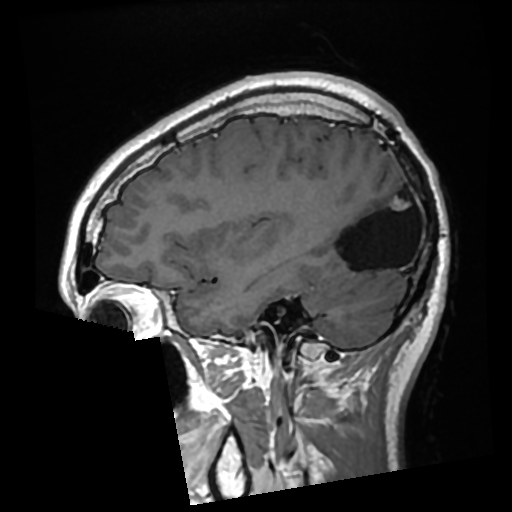
Brain MRI from a brain-tumour surgery series, one sagittal slice; position 91 of 276 along the scan axis; T1-weighted post-contrast; 0.7 mm slice thickness; 512 × 512 image matrix, field of view 250 × 250 mm. From the clinical record (not read from this slice): histopathology: Glioma with ependymal features; WHO grade: 2; tumour location: Left Parietal.
Structures marked on this image (manually delineated by an expert):
- previous resection cavity: bounding box <328,182,413,270> (left, top, right, bottom; pixels)
- tumour: <391,199,409,211>